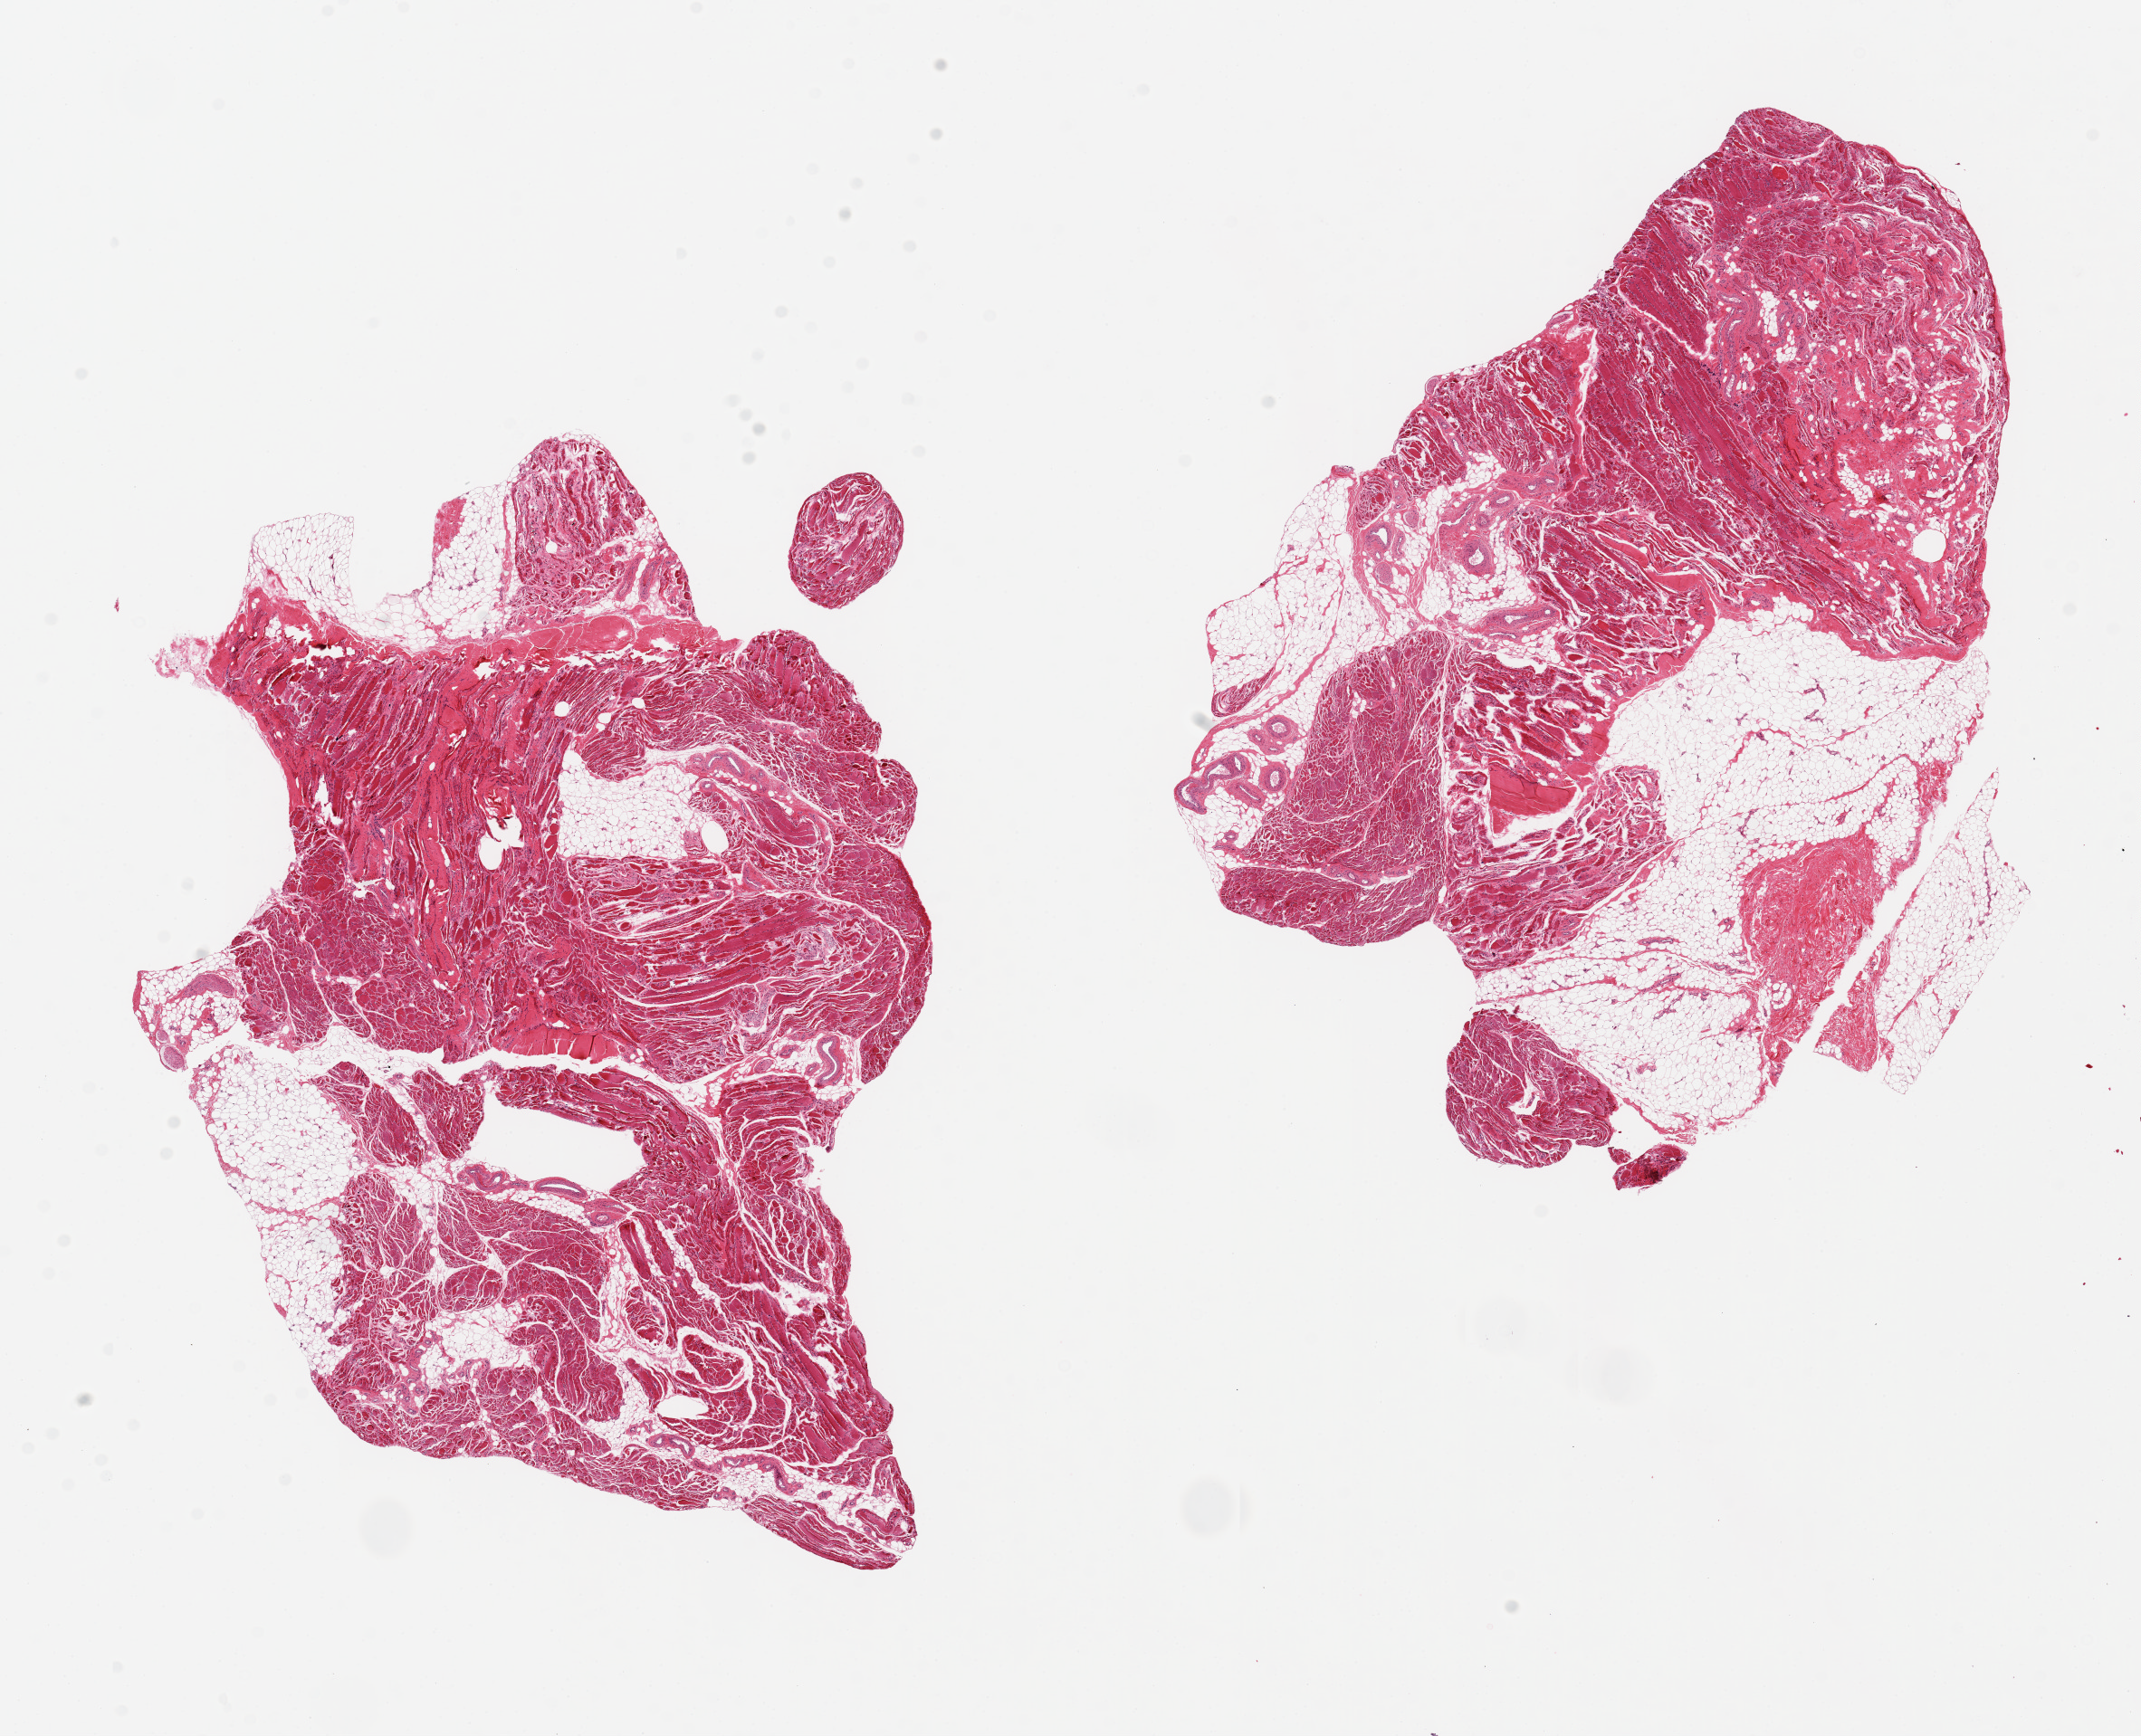
Digitized haematoxylin and eosin-stained section, low-resolution overview of the scanned area, about 18.7 x 15.2 mm (from a 20x scan); PAXgene-fixed, paraffin-embedded tissue; sampled site (target tissue): skeletal muscle; tissue donor sample. Male donor.
Pathologist's review note for this sample: 2 pieces, 10x7 & 9.5x8mm; Fatty infiltration, fibrosis and irregular fiber size c/w atrophy. 30% adipose.